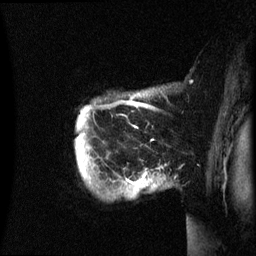
Breast MRI (dynamic contrast-enhanced), one sagittal slice. Slice 54 of 60 in the series (ordered by position). Dynamic contrast-enhanced series, image 2 of 3 at this slice position (ordered by acquisition). 1.5 T. TE 4.2 ms, TR 8.4 ms. 2.4 mm slice thickness. 256 × 256 image matrix. Female patient, age 49 years.
Structures marked on this image (semi-automatically segmented with operator editing):
- analysis volume of interest (the breast-tissue region the enhancement analysis was run in; not a lesion): bounding box [x1, y1, x2, y2] px = [75, 90, 169, 199]
- tumour enhancement mask (voxels above the 70 % enhancement threshold inside the analysis volume of interest): [126, 173, 146, 184]